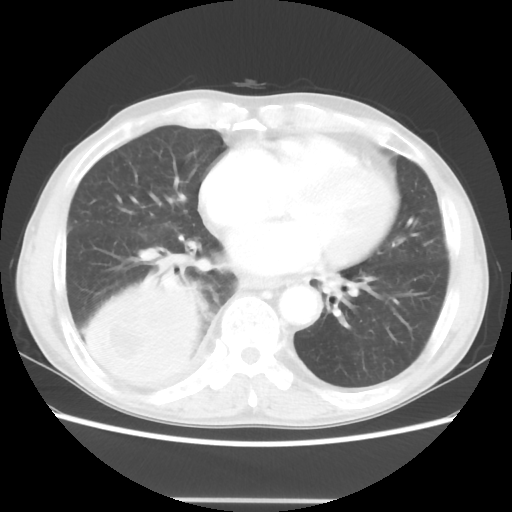
Chest CT, one axial slice. Position 16 of 48 along the scan axis. 100 kVp. Lung window (W 1500 / L -600 HU). 5 mm slice thickness. 512 × 512 image matrix, field of view 361 × 361 mm. Patient: male, 66 years. From the clinical record (not read from this slice): clinical TNM (as recorded): T4 N1 M1; histopathological grade: G3.
Annotated regions visible in this slice (rectangle marked by the reading radiologist):
- lung tumour (recorded histology: small cell carcinoma): bounding box <69,267,210,390> (left, top, right, bottom; pixels)